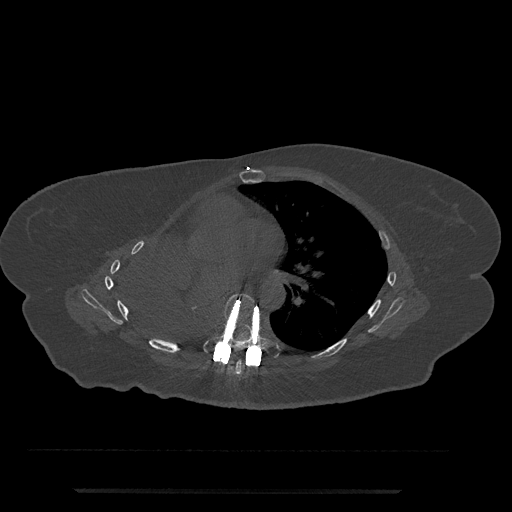
CT including the spine, one axial slice. Slice 452 of 797 in the series (ordered by position). Reconstruction kernel Br40s/3. 120 kVp. Bone window (W 1800 / L 400 HU). 0.5 mm slice thickness. 512 × 512 image matrix, field of view 440 × 440 mm. Patient: female, 51 years. From the clinical record (not read from this slice): primary cancer: neuro.
Structures marked on this image (semi-automatically segmented with operator editing):
- T6 vertebra: bounding box (x1, y1, x2, y2) in pixels: (221, 359, 243, 377)
- T7 vertebra: (203, 294, 280, 357)